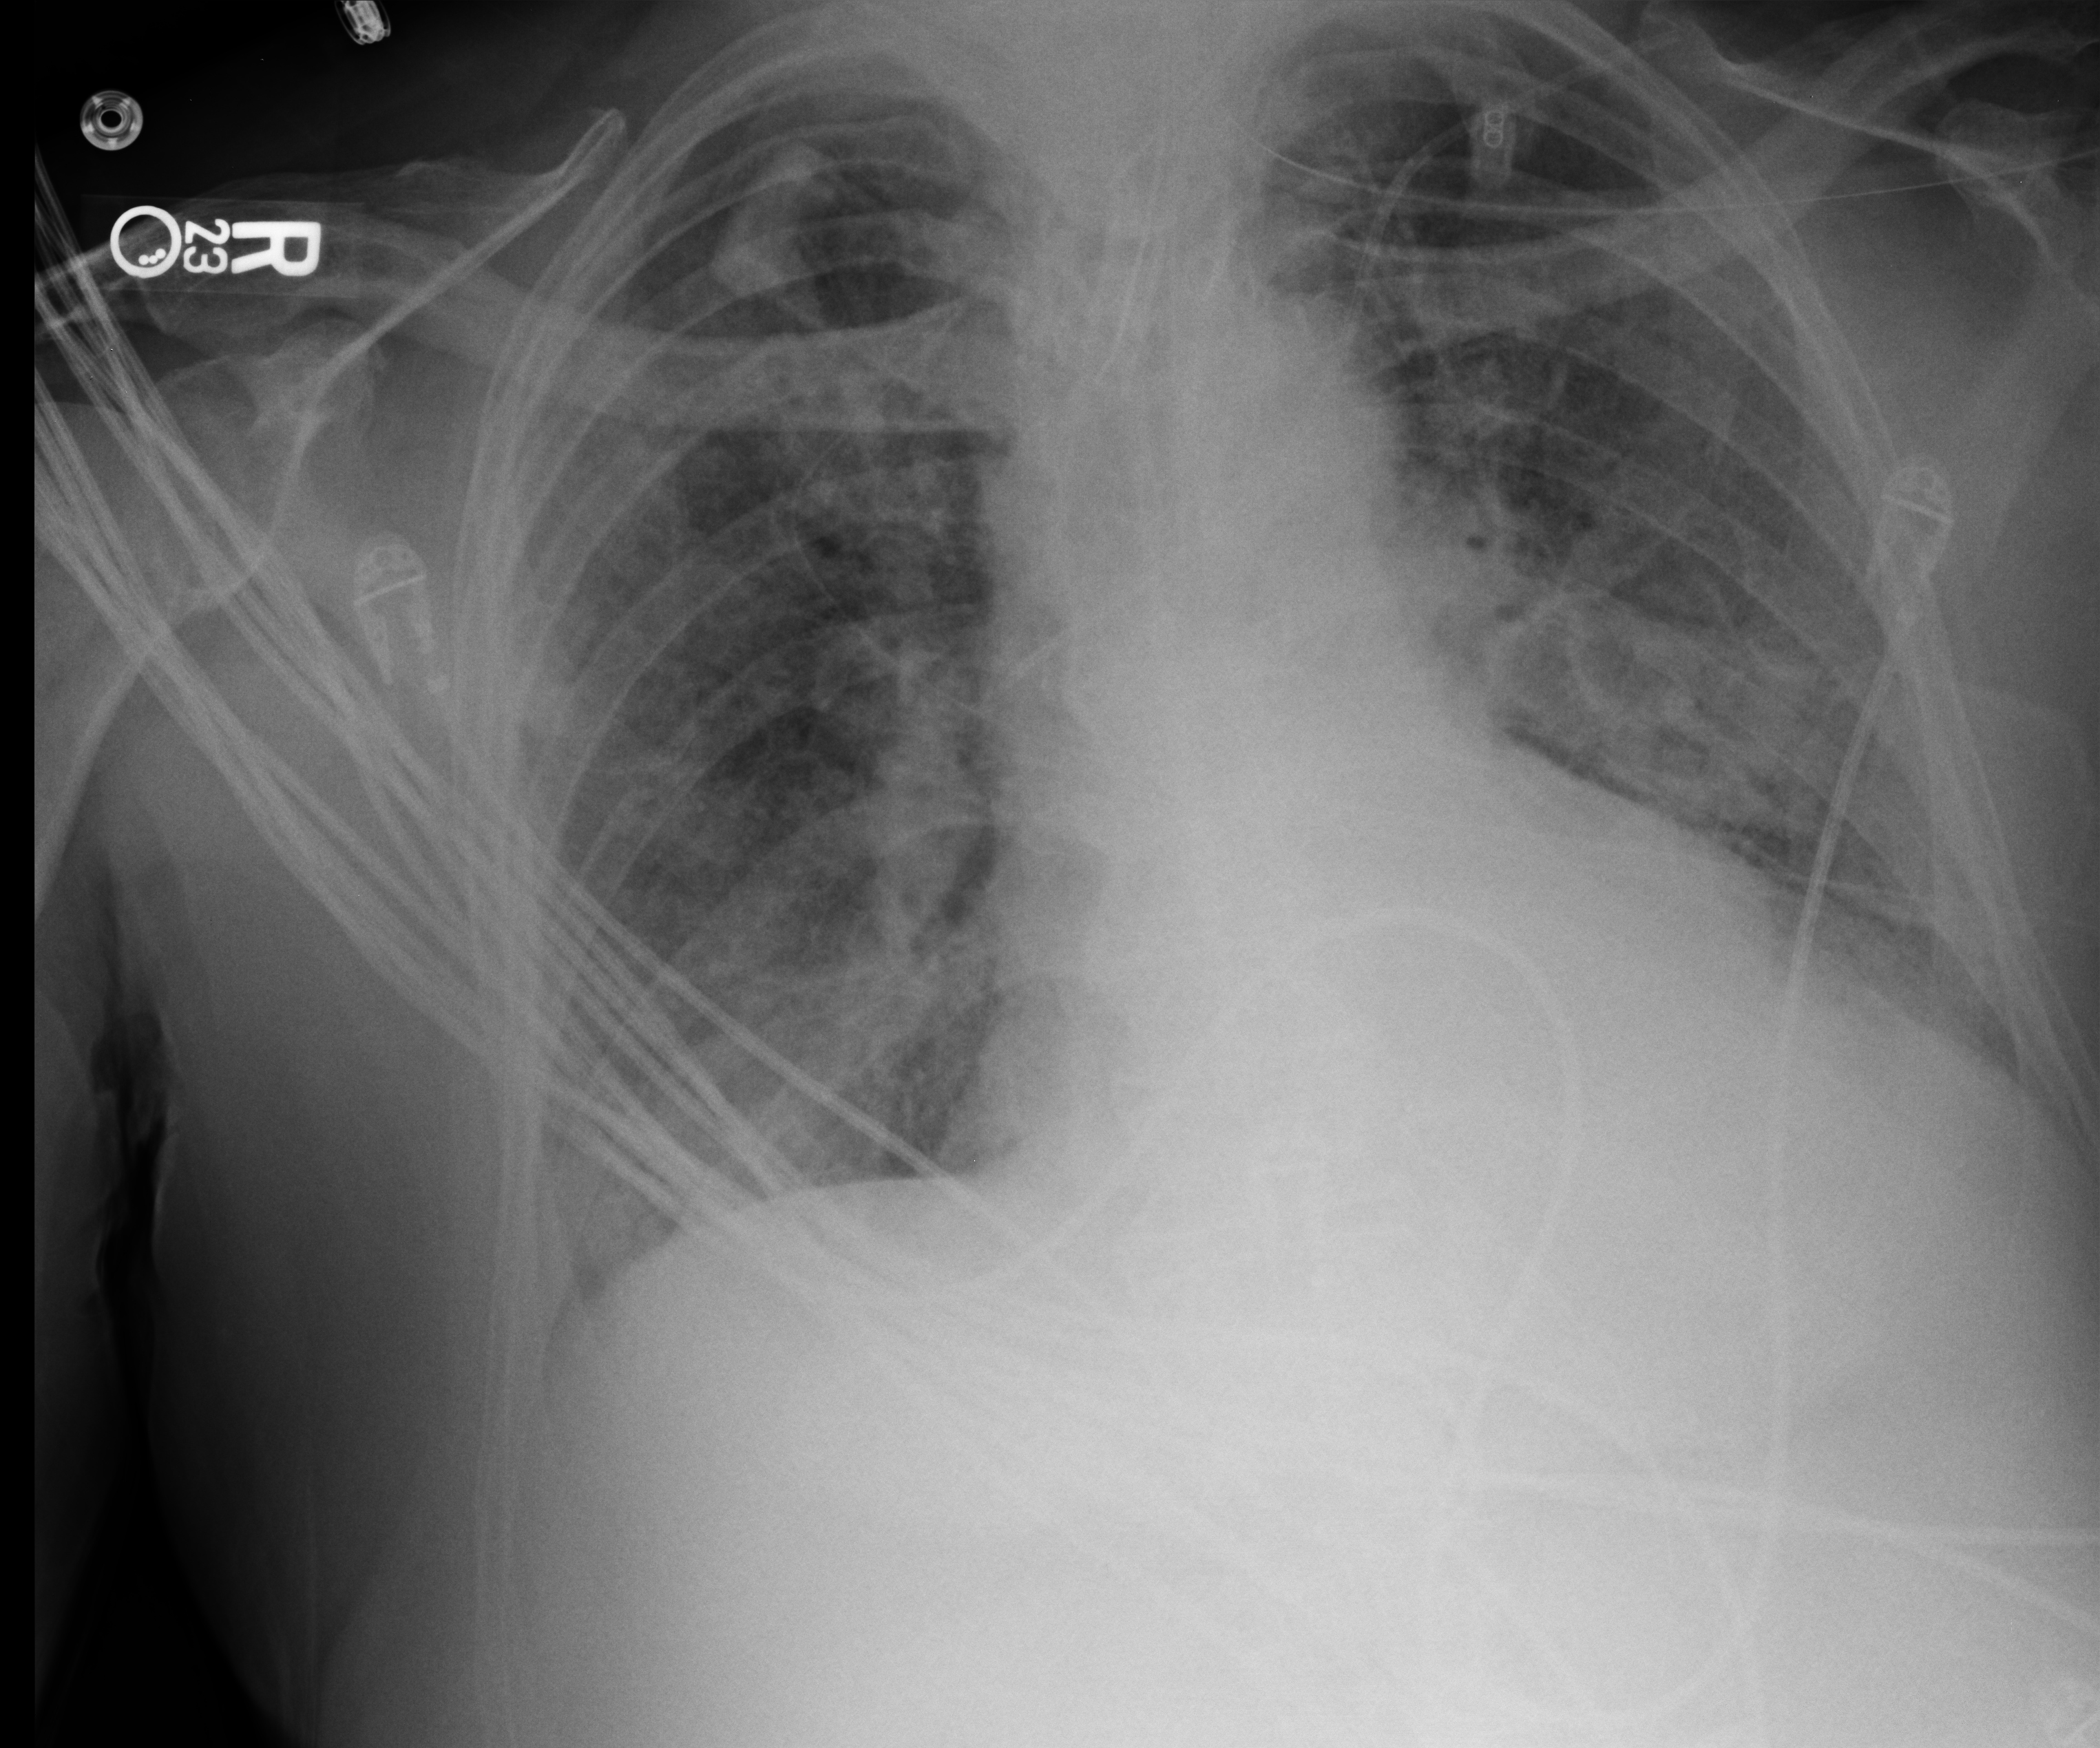
Bedside chest radiograph (computed radiography); anteroposterior (AP) projection. Male patient hospitalised with COVID-19, age 75–90 years.
From the hospital-stay record, not from the radiograph (when in the stay this image was taken is not recorded): diabetes (admission record): no; mechanically ventilated during this hospital stay: yes.